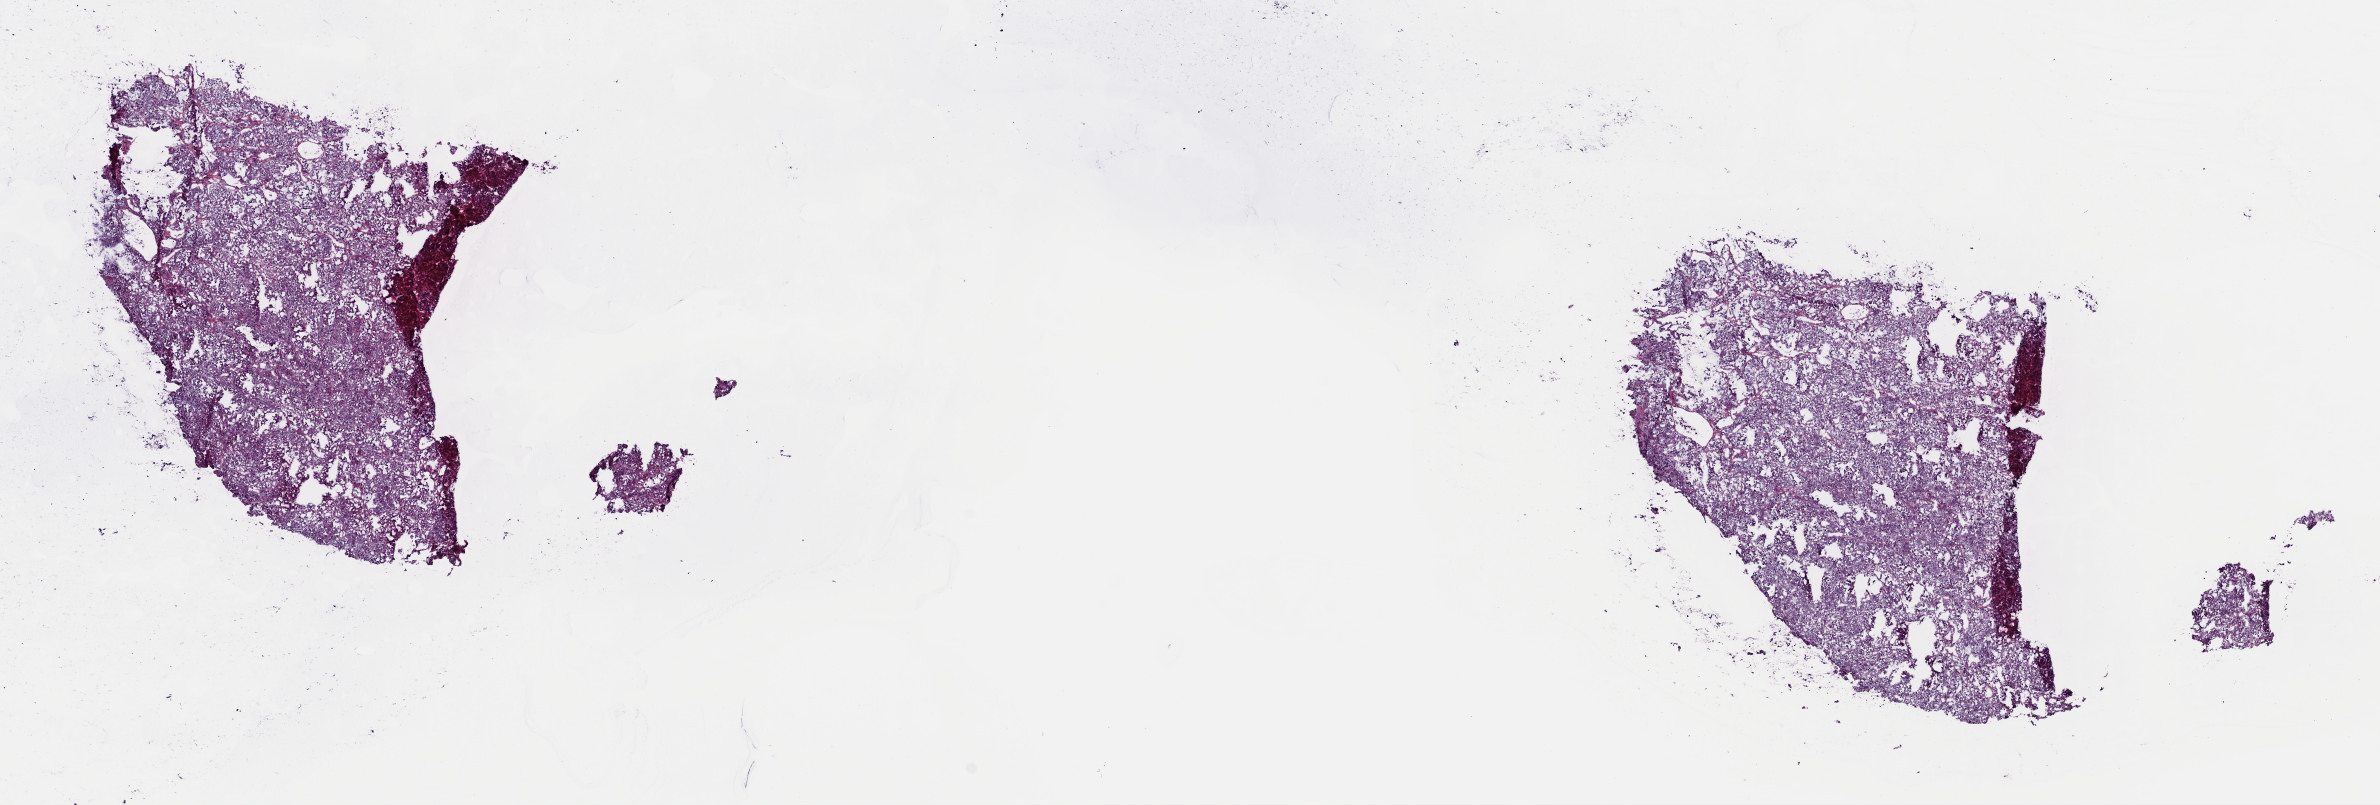
H&E whole-slide image — whole scanned area (about 18.8 x 6.4 mm) shown as a low-resolution overview. Frozen section from the top of the tissue portion. Primary tumour sample from the adrenal cortex. Patient: female, age at initial diagnosis 75 years. Composition of this section per pathologist review: tumour cells 98%, tumour nuclei 98%, normal cells 0%, stromal cells 2%, necrosis 0%. Inflammatory infiltration, as recorded: lymphocyte infiltration 0%, monocyte infiltration 0%, neutrophil infiltration 0%.
Pathologic diagnosis: Adrenal cortical carcinoma (cortex of adrenal gland). Lymph nodes positive (case pathology): 0 of 10 examined.